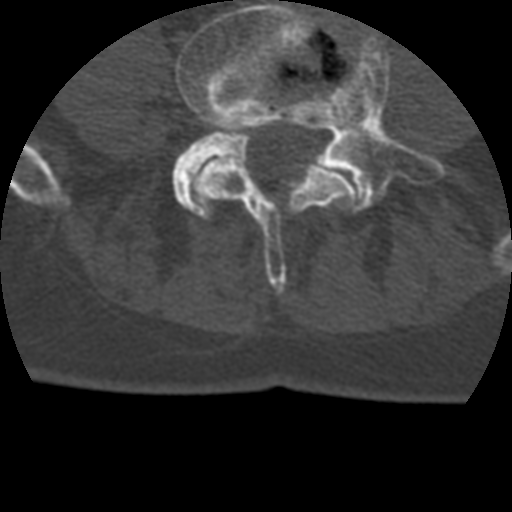
CT including the spine, one axial slice; slice 55 of 399 in the series (ordered by position); bone window (W 1800 / L 400 HU); 1.25 mm slice thickness; 512 × 512 image matrix, field of view 160 × 160 mm. Patient age 69 years. From the clinical record (not read from this slice): primary cancer: prostate.
Outlined on this slice (semi-automatic segmentation, software-assisted and operator-edited):
- L4 vertebra: bounding box <176,0,357,294> (left, top, right, bottom; pixels)
- L5 vertebra: <172,36,432,210>